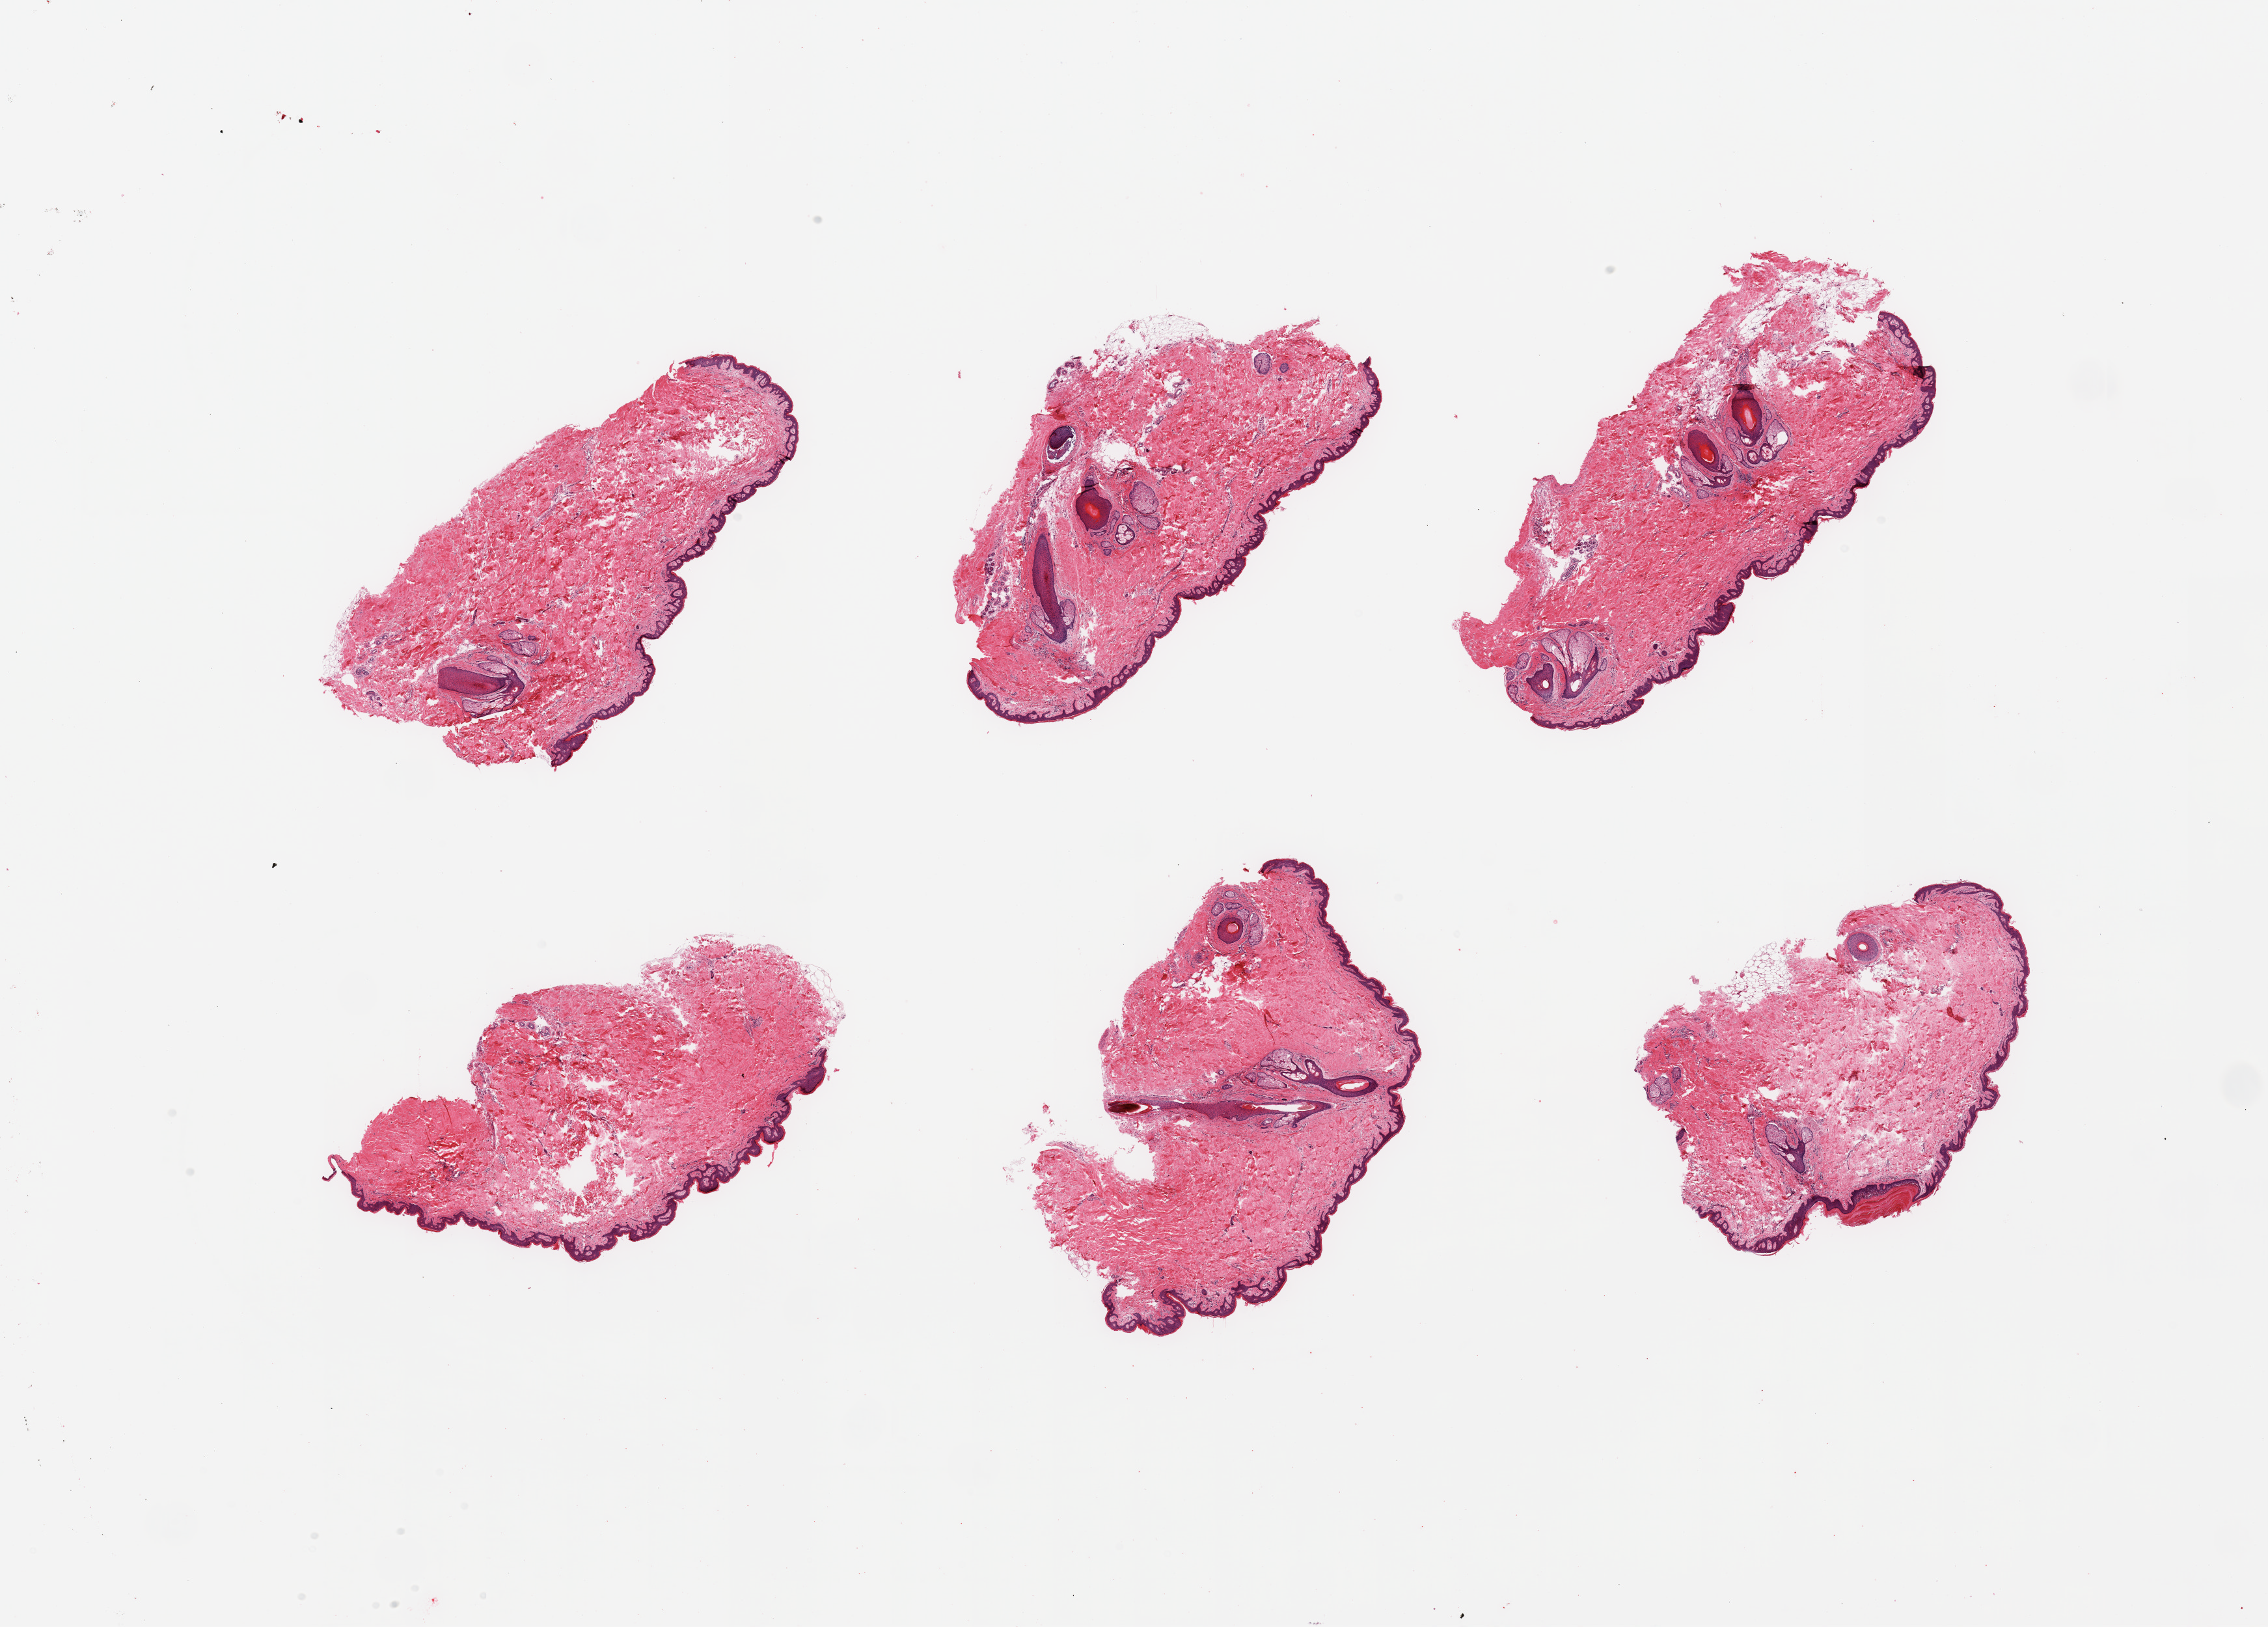
Whole-slide image, hematoxylin and eosin (H&E) stain, brightfield — a low-resolution overview of the entire scanned area, about 27.6 x 19.8 mm. PAXgene-fixed, paraffin-embedded tissue. Target tissue: skin of suprapubic region. Tissue donor sample. Donor: male.
Review note (as recorded): 6 pieces, minimal dermal fat, squamous epithelium is ~30-60 microns.